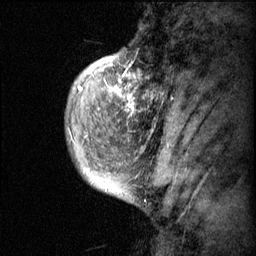
Breast MRI (dynamic contrast-enhanced), one sagittal slice. Slice 11 of 60 in the series (ordered by position). Dynamic contrast-enhanced series, image 2 of 3 at this slice position (ordered by acquisition). 1.5 T. TE 4.2 ms, TR 11.1 ms. 2 mm slice thickness. 256 × 256 image matrix, field of view 180 × 180 mm. Female patient, age 50 years.
Annotated regions visible in this slice (semi-automatic segmentation, software-assisted and operator-edited):
- analysis volume of interest (the breast-tissue region the enhancement analysis was run in; not a lesion): bounding box <82,56,168,143> (left, top, right, bottom; pixels)
- tumour enhancement mask (voxels above the 70 % enhancement threshold inside the analysis volume of interest): <82,56,168,143>